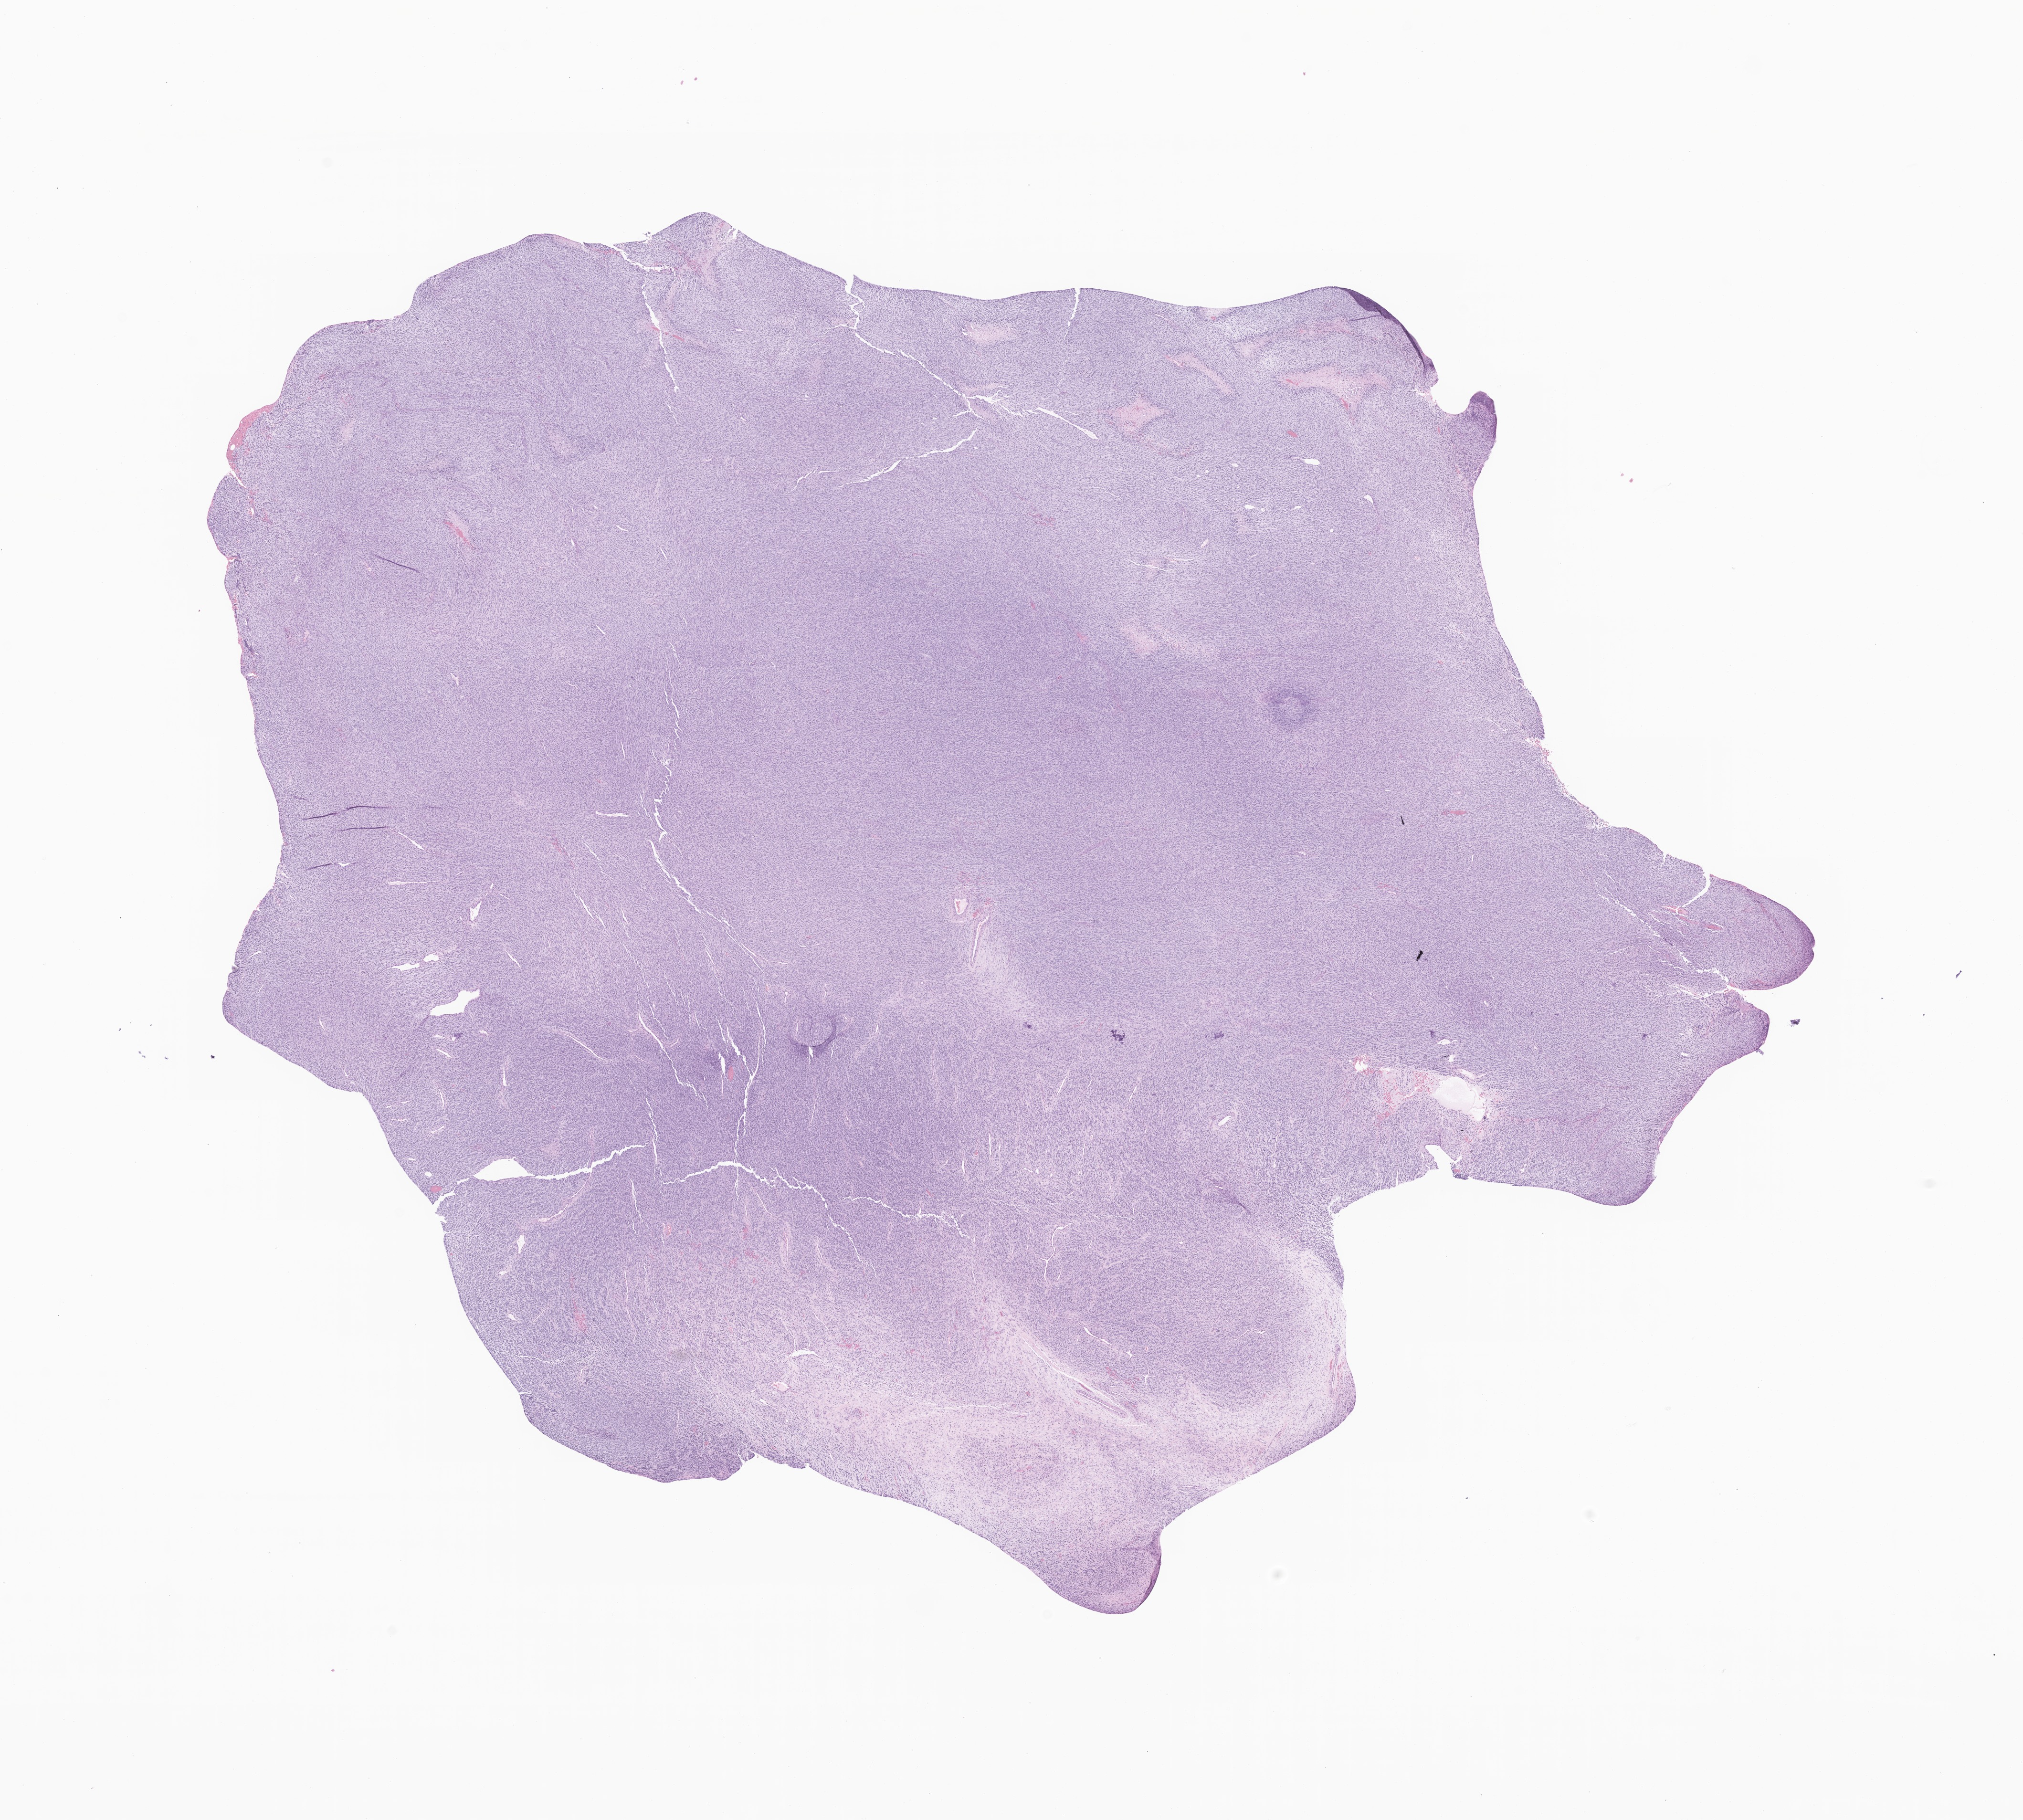
Haematoxylin and eosin whole-slide image of tumor tissue from the soft tissue of thorax, low-resolution overview of the scanned area, about 17.9 x 16.1 mm, FFPE section. Patient: male, age 66 days.
Diagnosis: Malignant tumor, spindle cell type. Tissue or organ of origin (case record): connective, subcutaneous and other soft tissues of thorax.